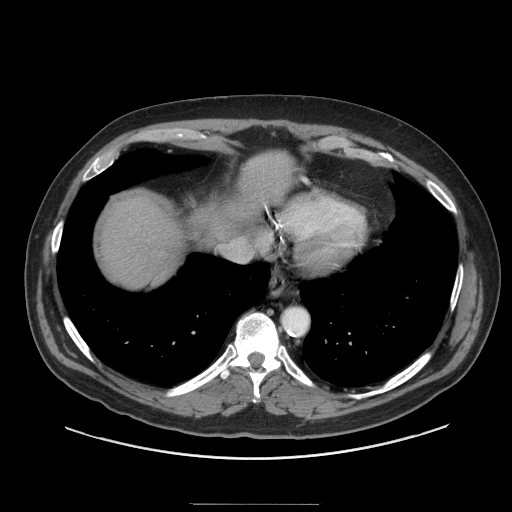
Contrast-enhanced abdominal CT (liver protocol), one axial slice; slice 83 of 91 in the series (ordered by position); reconstruction kernel STANDARD; 140 kVp; soft-tissue window (W 400 / L 40 HU); 2.5 mm slice thickness; 512 × 512 image matrix, field of view 440 × 440 mm. From the clinical record (not read from this slice): diagnosis: hepatocellular carcinoma (patient treated with transarterial chemoembolisation; whether this scan precedes or follows treatment is not stated here); TNM stage (as recorded): Stage-I; Child-Pugh class: A; tumour differentiation: well differentiated.
Annotated regions visible in this slice (semi-automatic segmentation, software-assisted and operator-edited):
- liver parenchyma outside the tumour (the mass and vessels are separate outlines, so this box may not span the whole liver): bounding box [x1, y1, x2, y2] px = [100, 152, 290, 288]